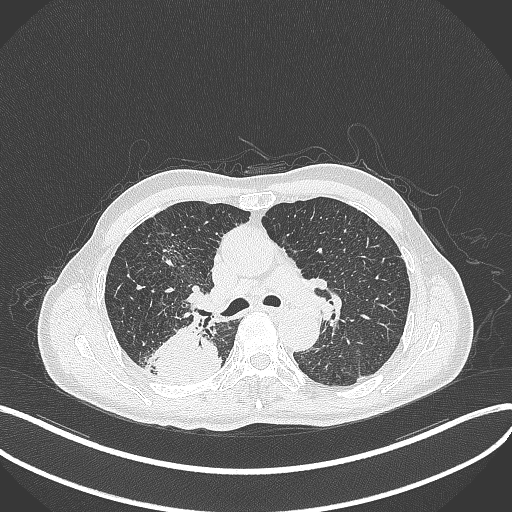
Chest CT, one axial slice. Slice 292 of 428 in the series (ordered by position). Reconstruction kernel B70f. Lung window (W 1500 / L -600 HU). 1 mm slice thickness. 512 × 512 image matrix. Male patient, age 79 years. Case-level facts recorded for this patient, not image findings: clinical TNM (as recorded): T3 N0 M0.
Structures marked on this image (bounding box drawn by a radiologist):
- lung tumour (recorded histology: adenocarcinoma): box from (x=153, y=328) to (x=222, y=385) px